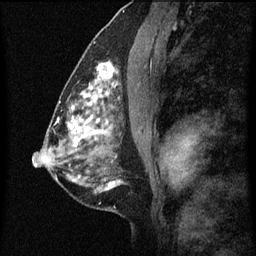
Breast MRI (dynamic contrast-enhanced), one sagittal slice; position 33 of 60 along the scan axis; dynamic contrast-enhanced series, image 2 of 7 at this slice position (ordered by acquisition); 1.5 T; TE 4.2 ms, TR 8 ms; 256 × 256 image matrix, field of view 180 × 180 mm. Patient: female, 51 years.
Structures marked on this image (semi-automatically segmented with operator editing):
- analysis volume of interest (the breast-tissue region the enhancement analysis was run in; not a lesion): bounding box (x1, y1, x2, y2) in pixels: (86, 48, 121, 101)
- tumour enhancement mask (voxels above the 70 % enhancement threshold inside the analysis volume of interest): (86, 64, 115, 101)